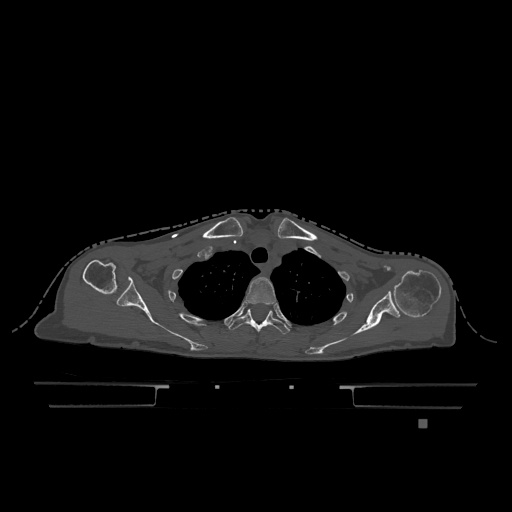
CT including the spine, one axial slice. Bone window (W 1800 / L 400 HU). 0.5 mm slice thickness. 512 × 512 image matrix, field of view 500 × 500 mm. Female patient, age 74 years. Case-level facts recorded for this patient, not image findings: primary cancer: lung; vertebrae with lytic lesions (as recorded): T1, T4, T5, T6, L4, L5.
Structures marked on this image (semi-automatic segmentation, software-assisted and operator-edited):
- T2 vertebra: bounding box <245,277,276,305> (left, top, right, bottom; pixels)
- T3 vertebra: <229,309,290,334>